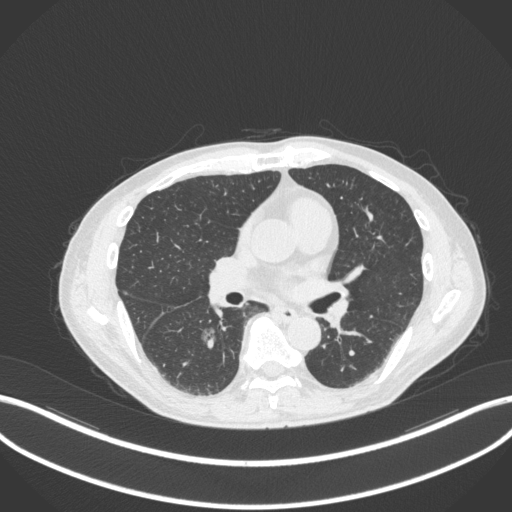
Chest CT, one axial slice; slice 168 of 324 in the series (ordered by position); lung window (W 1500 / L -600 HU); 512 × 512 image matrix. Patient: male, 61 years. Case-level facts recorded for this patient, not image findings: clinical TNM (as recorded): T1c N0 M0.
Structures marked on this image (rectangle marked by the reading radiologist):
- lung tumour (recorded histology: adenocarcinoma): bounding box (x1, y1, x2, y2) in pixels: (198, 323, 217, 353)